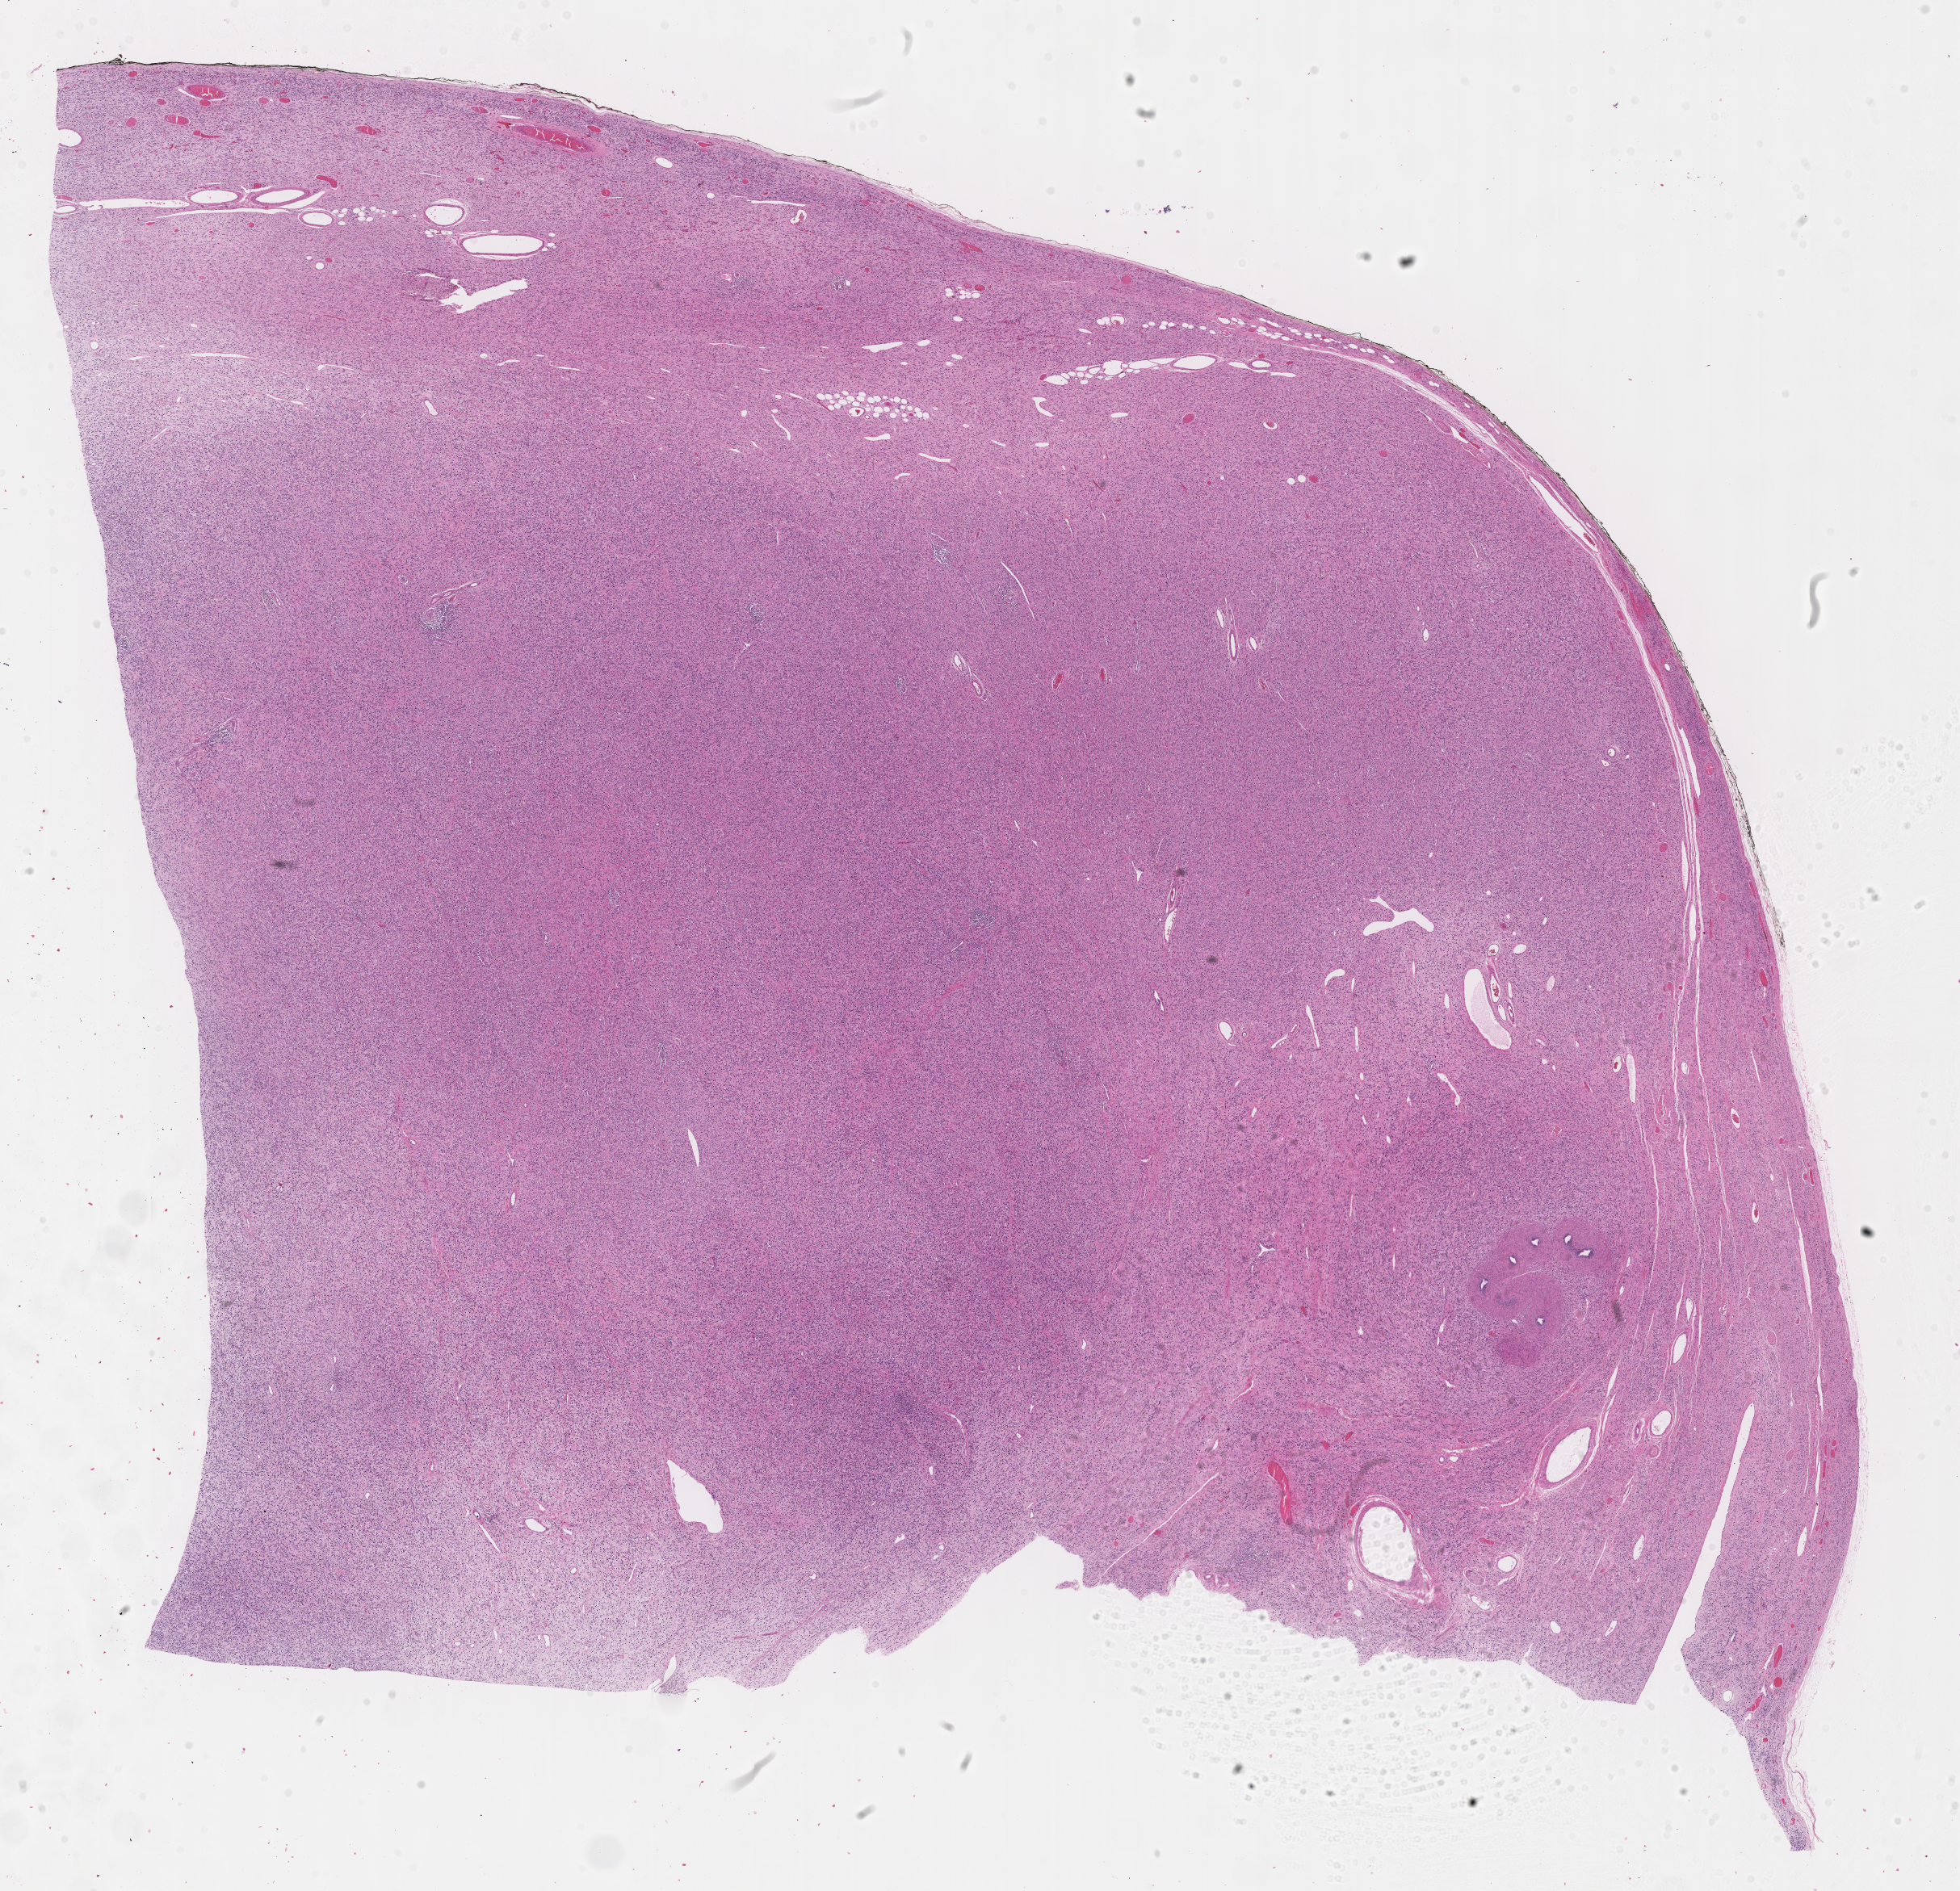
Digitized H&E-stained section of tumor tissue — low-resolution overview of the scanned area, about 19.6 x 18.9 mm; formalin-fixed paraffin-embedded section; site: testicle-left. Patient: male, age 9.3 years at diagnosis.
• stage (as recorded): 1
• primary site (case record): testis-Paratestis
• metastatic status at presentation (as recorded): non-metastatic
• diagnosis: rhabdomyosarcoma; histological classification: embryonal rhabdomyosarcoma